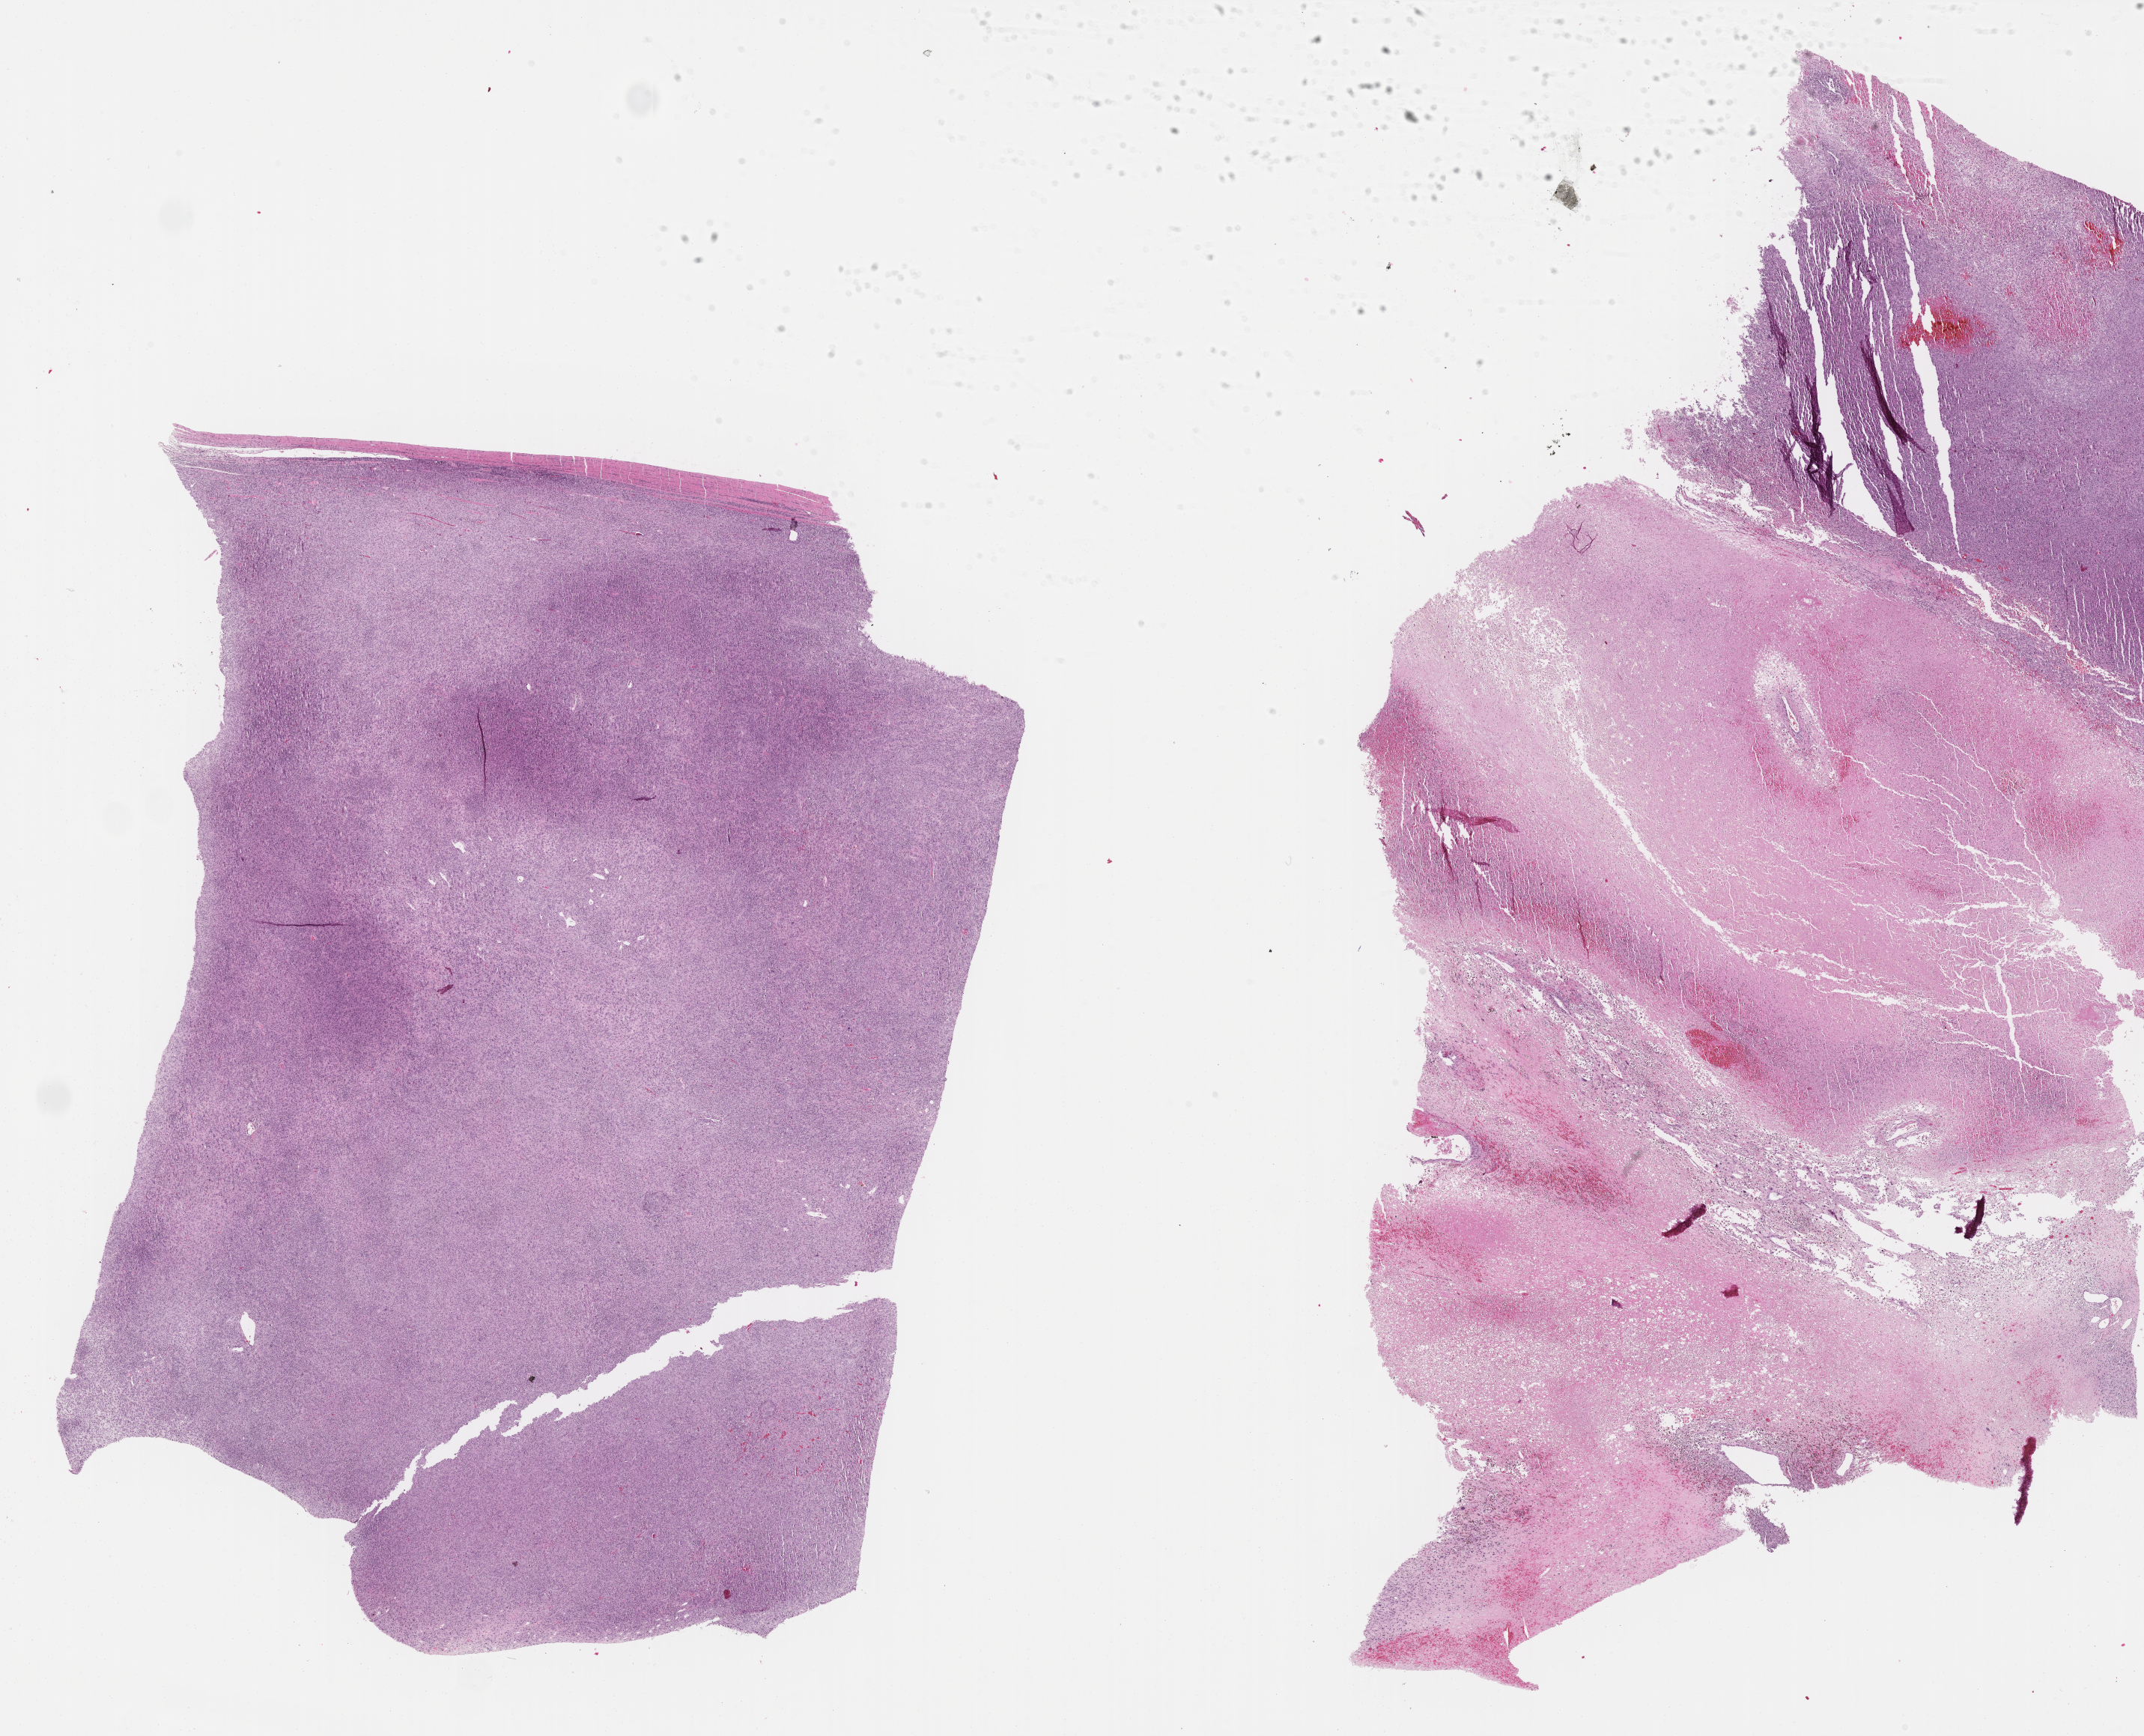
Digitized Hematoxylin and eosin (H&E) stained tissue section (whole slide), whole scanned area (about 23.0 x 18.6 mm) shown as a low-resolution overview. Formalin-fixed paraffin-embedded (FFPE) diagnostic section. Connective, subcutaneous and other soft tissues, primary tumour sample. Patient: male, age at initial diagnosis 85 years.
Diagnosis: Malignant fibrous histiocytoma (connective, subcutaneous and other soft tissues of lower limb and hip).